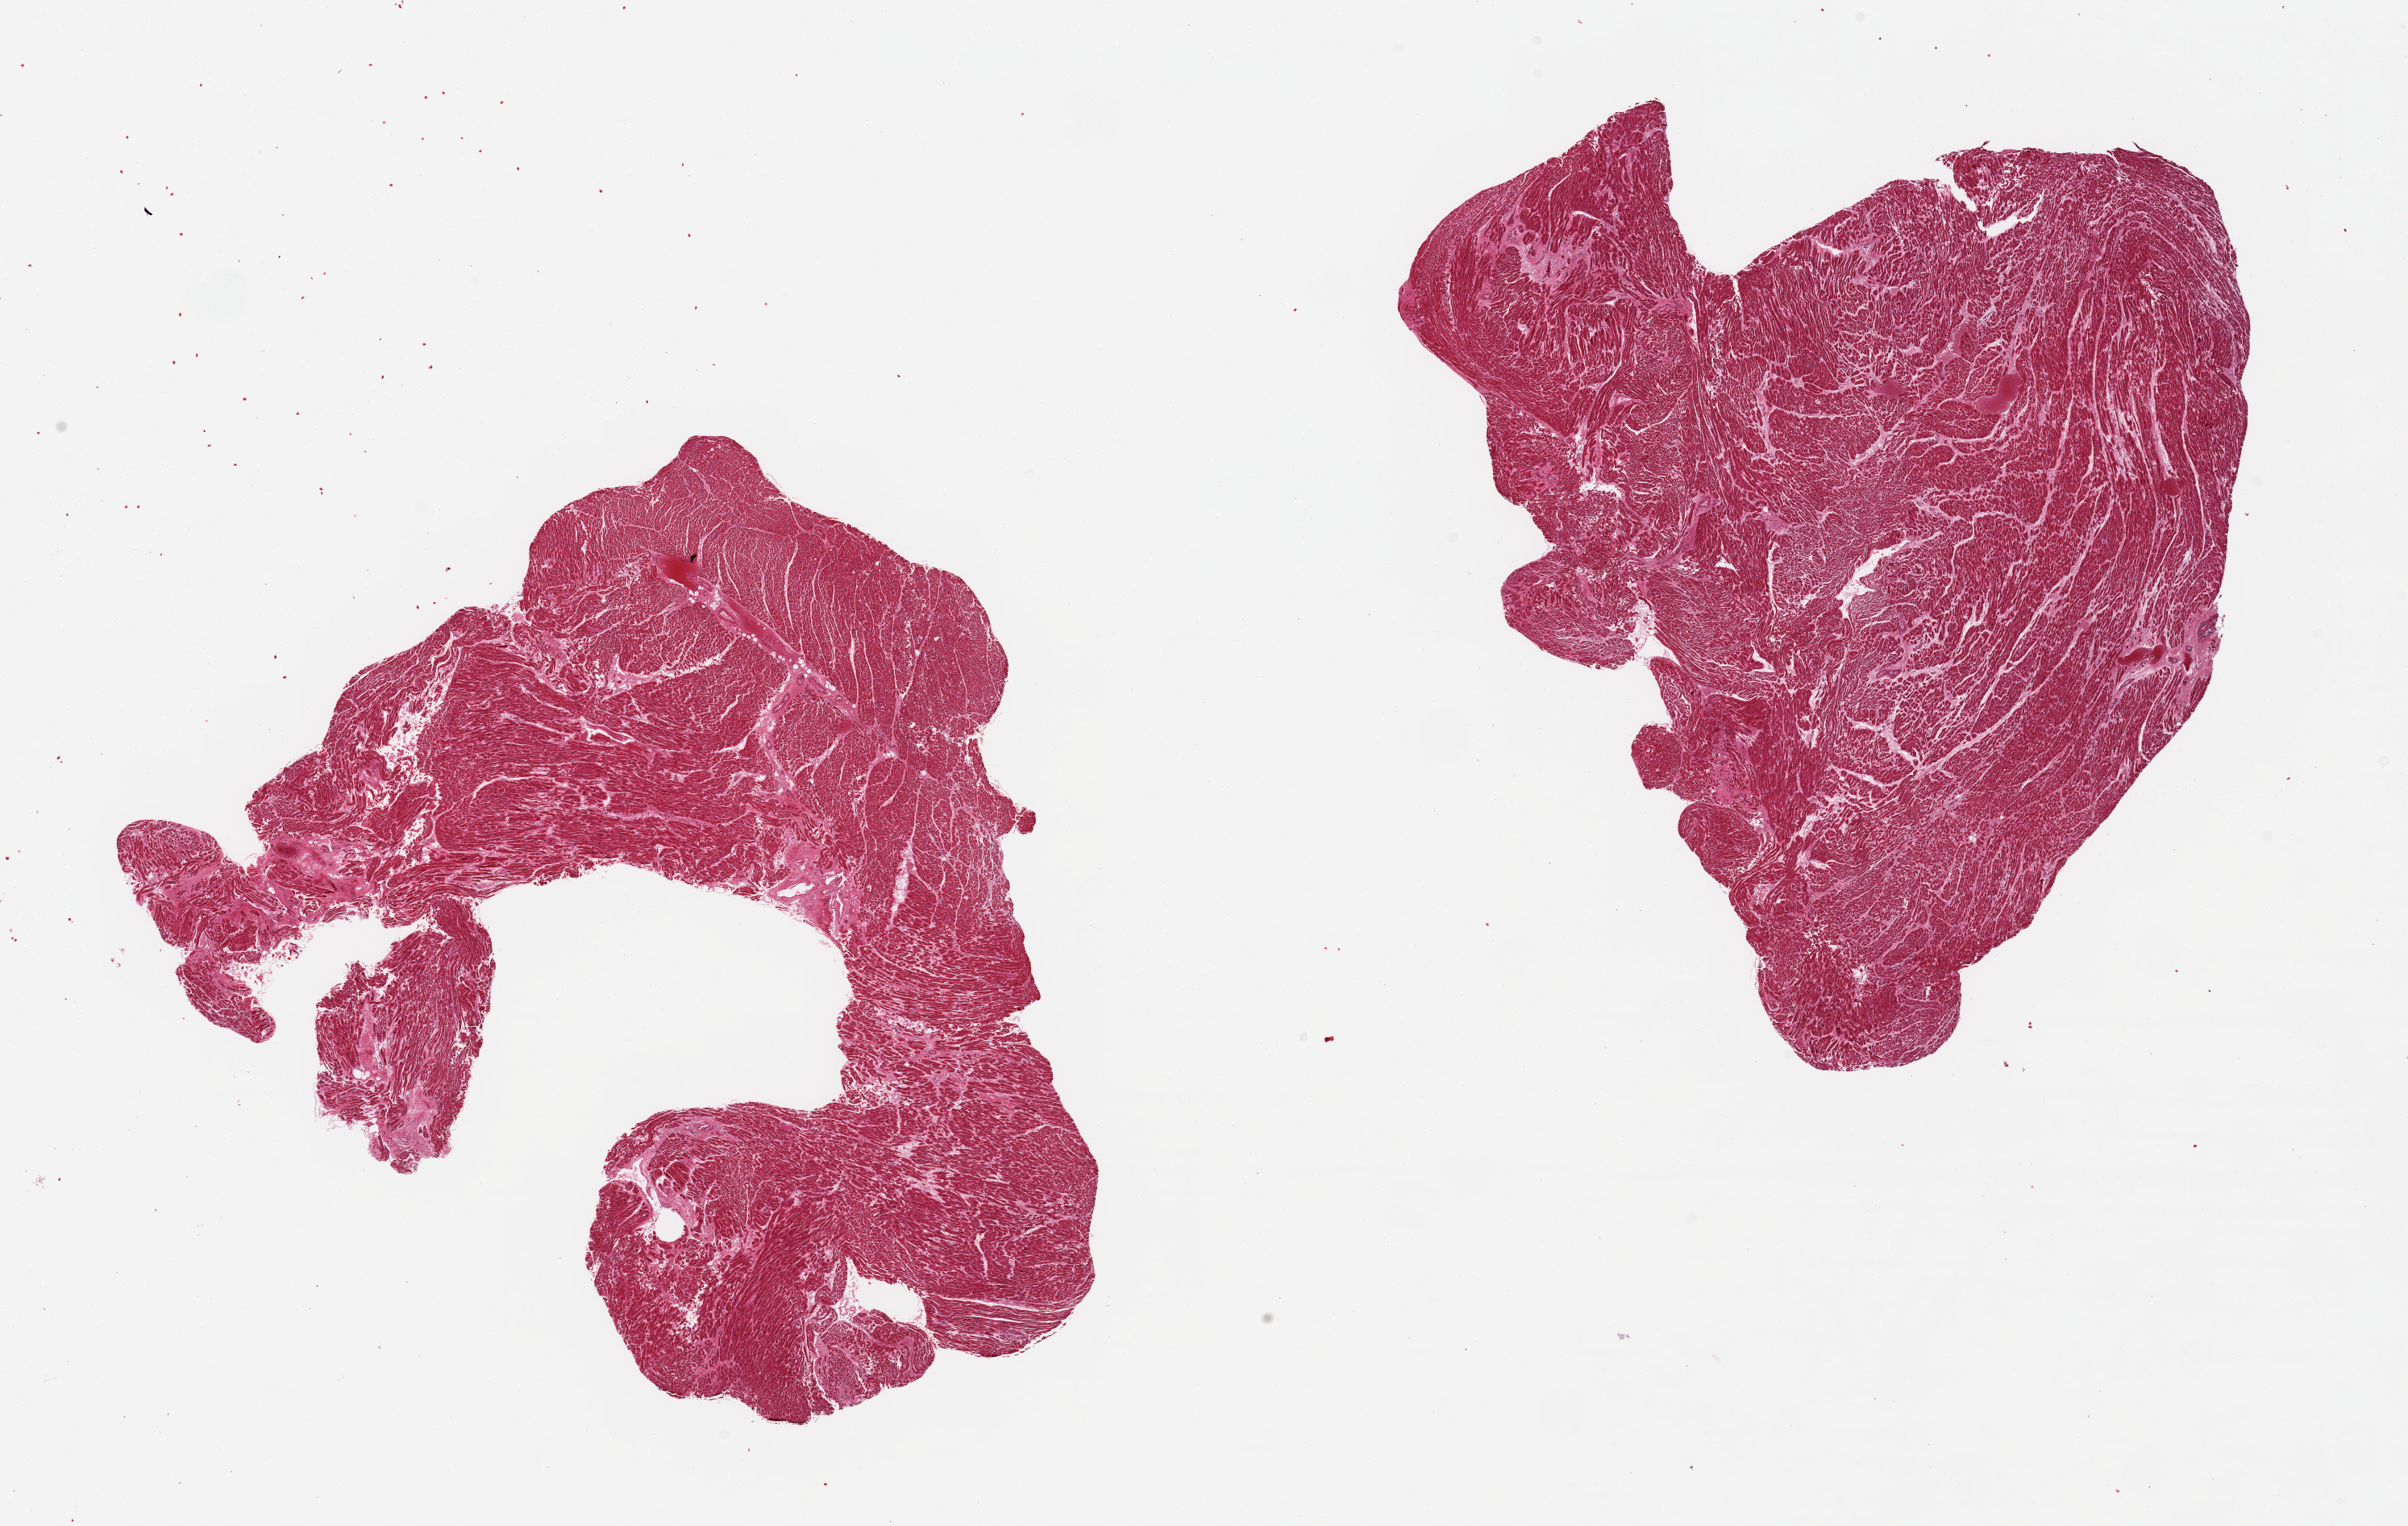
Whole-slide image, H&E stain, brightfield, a low-resolution overview of the entire scanned area, about 23.6 x 15.0 mm (acquisition: 20x scan); PAXgene-fixed paraffin-embedded (PFPE) section; section of heart (target tissue); tissue donor sample. Female donor.
• pathologist's review note for this sample: 2 pieces; interstitial and patchy fibrosis